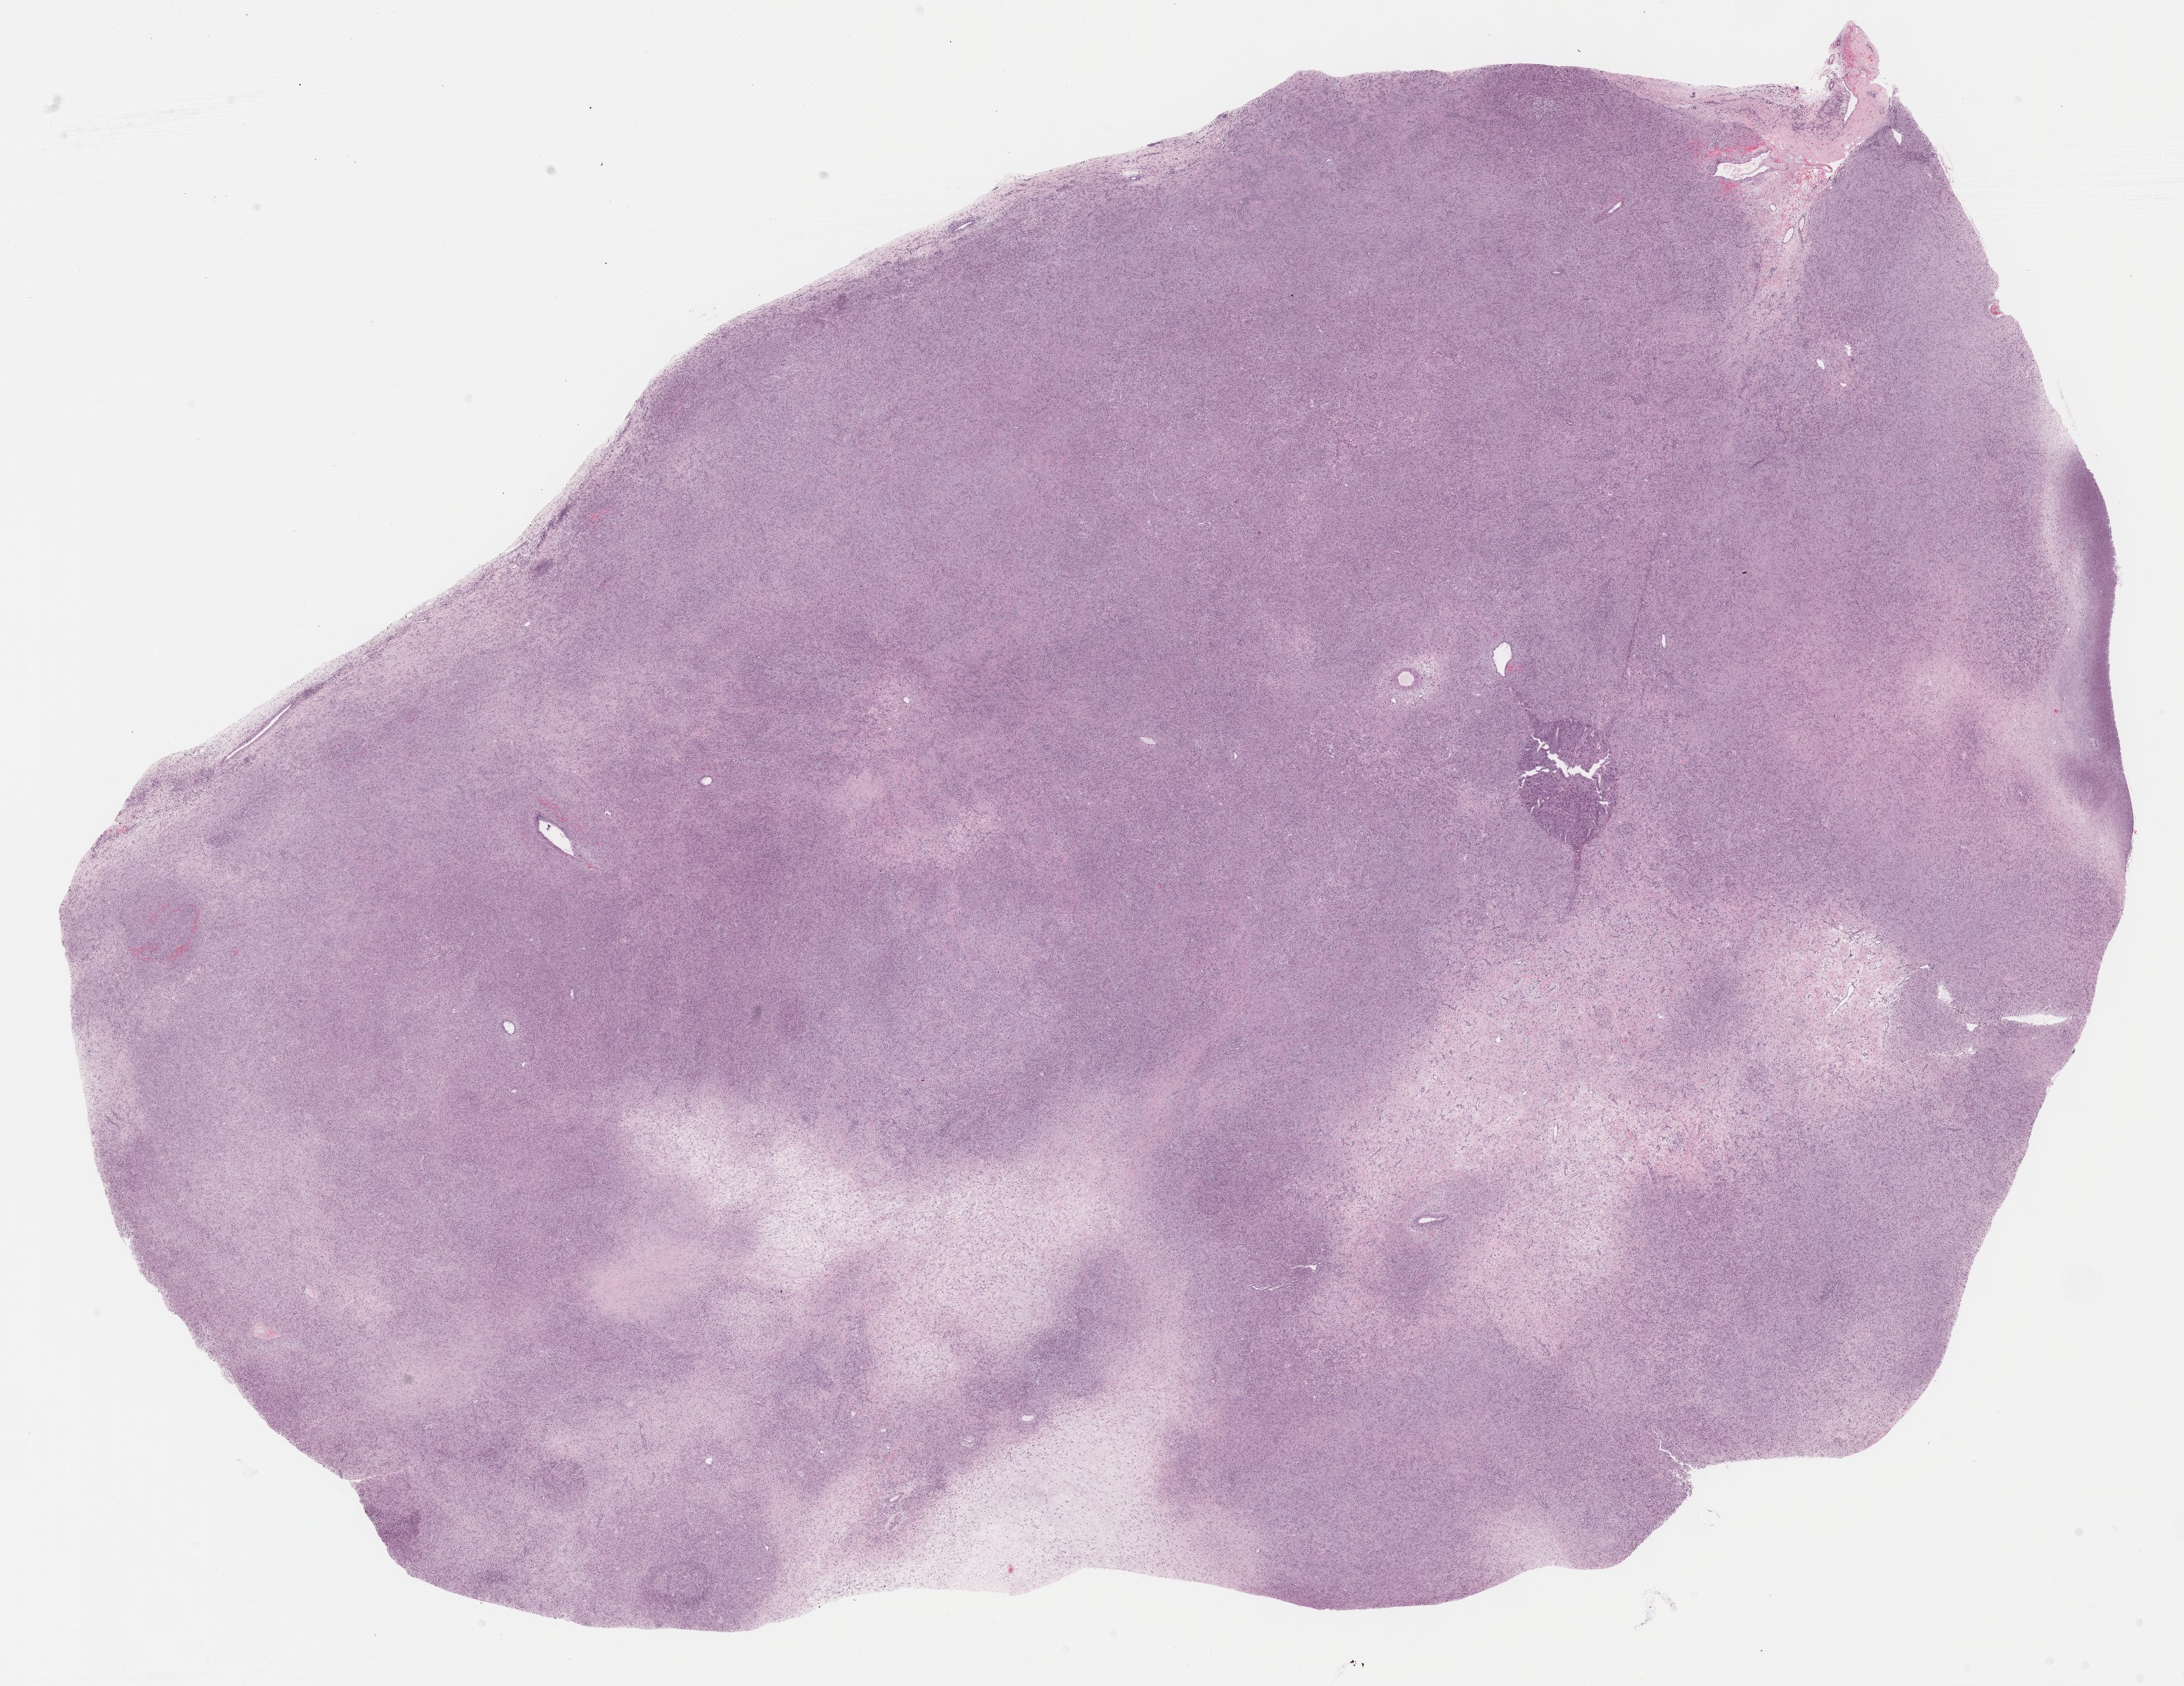
Whole-slide histology image, H&E-stained — shown as a low-resolution overview of the whole scanned area (about 25.7 x 19.8 mm), formalin-fixed paraffin-embedded (FFPE) diagnostic section, retroperitoneum and peritoneum, primary tumour sample. Patient: male, age at initial diagnosis 82 years.
* histologic diagnosis: Dedifferentiated liposarcoma (retroperitoneum)